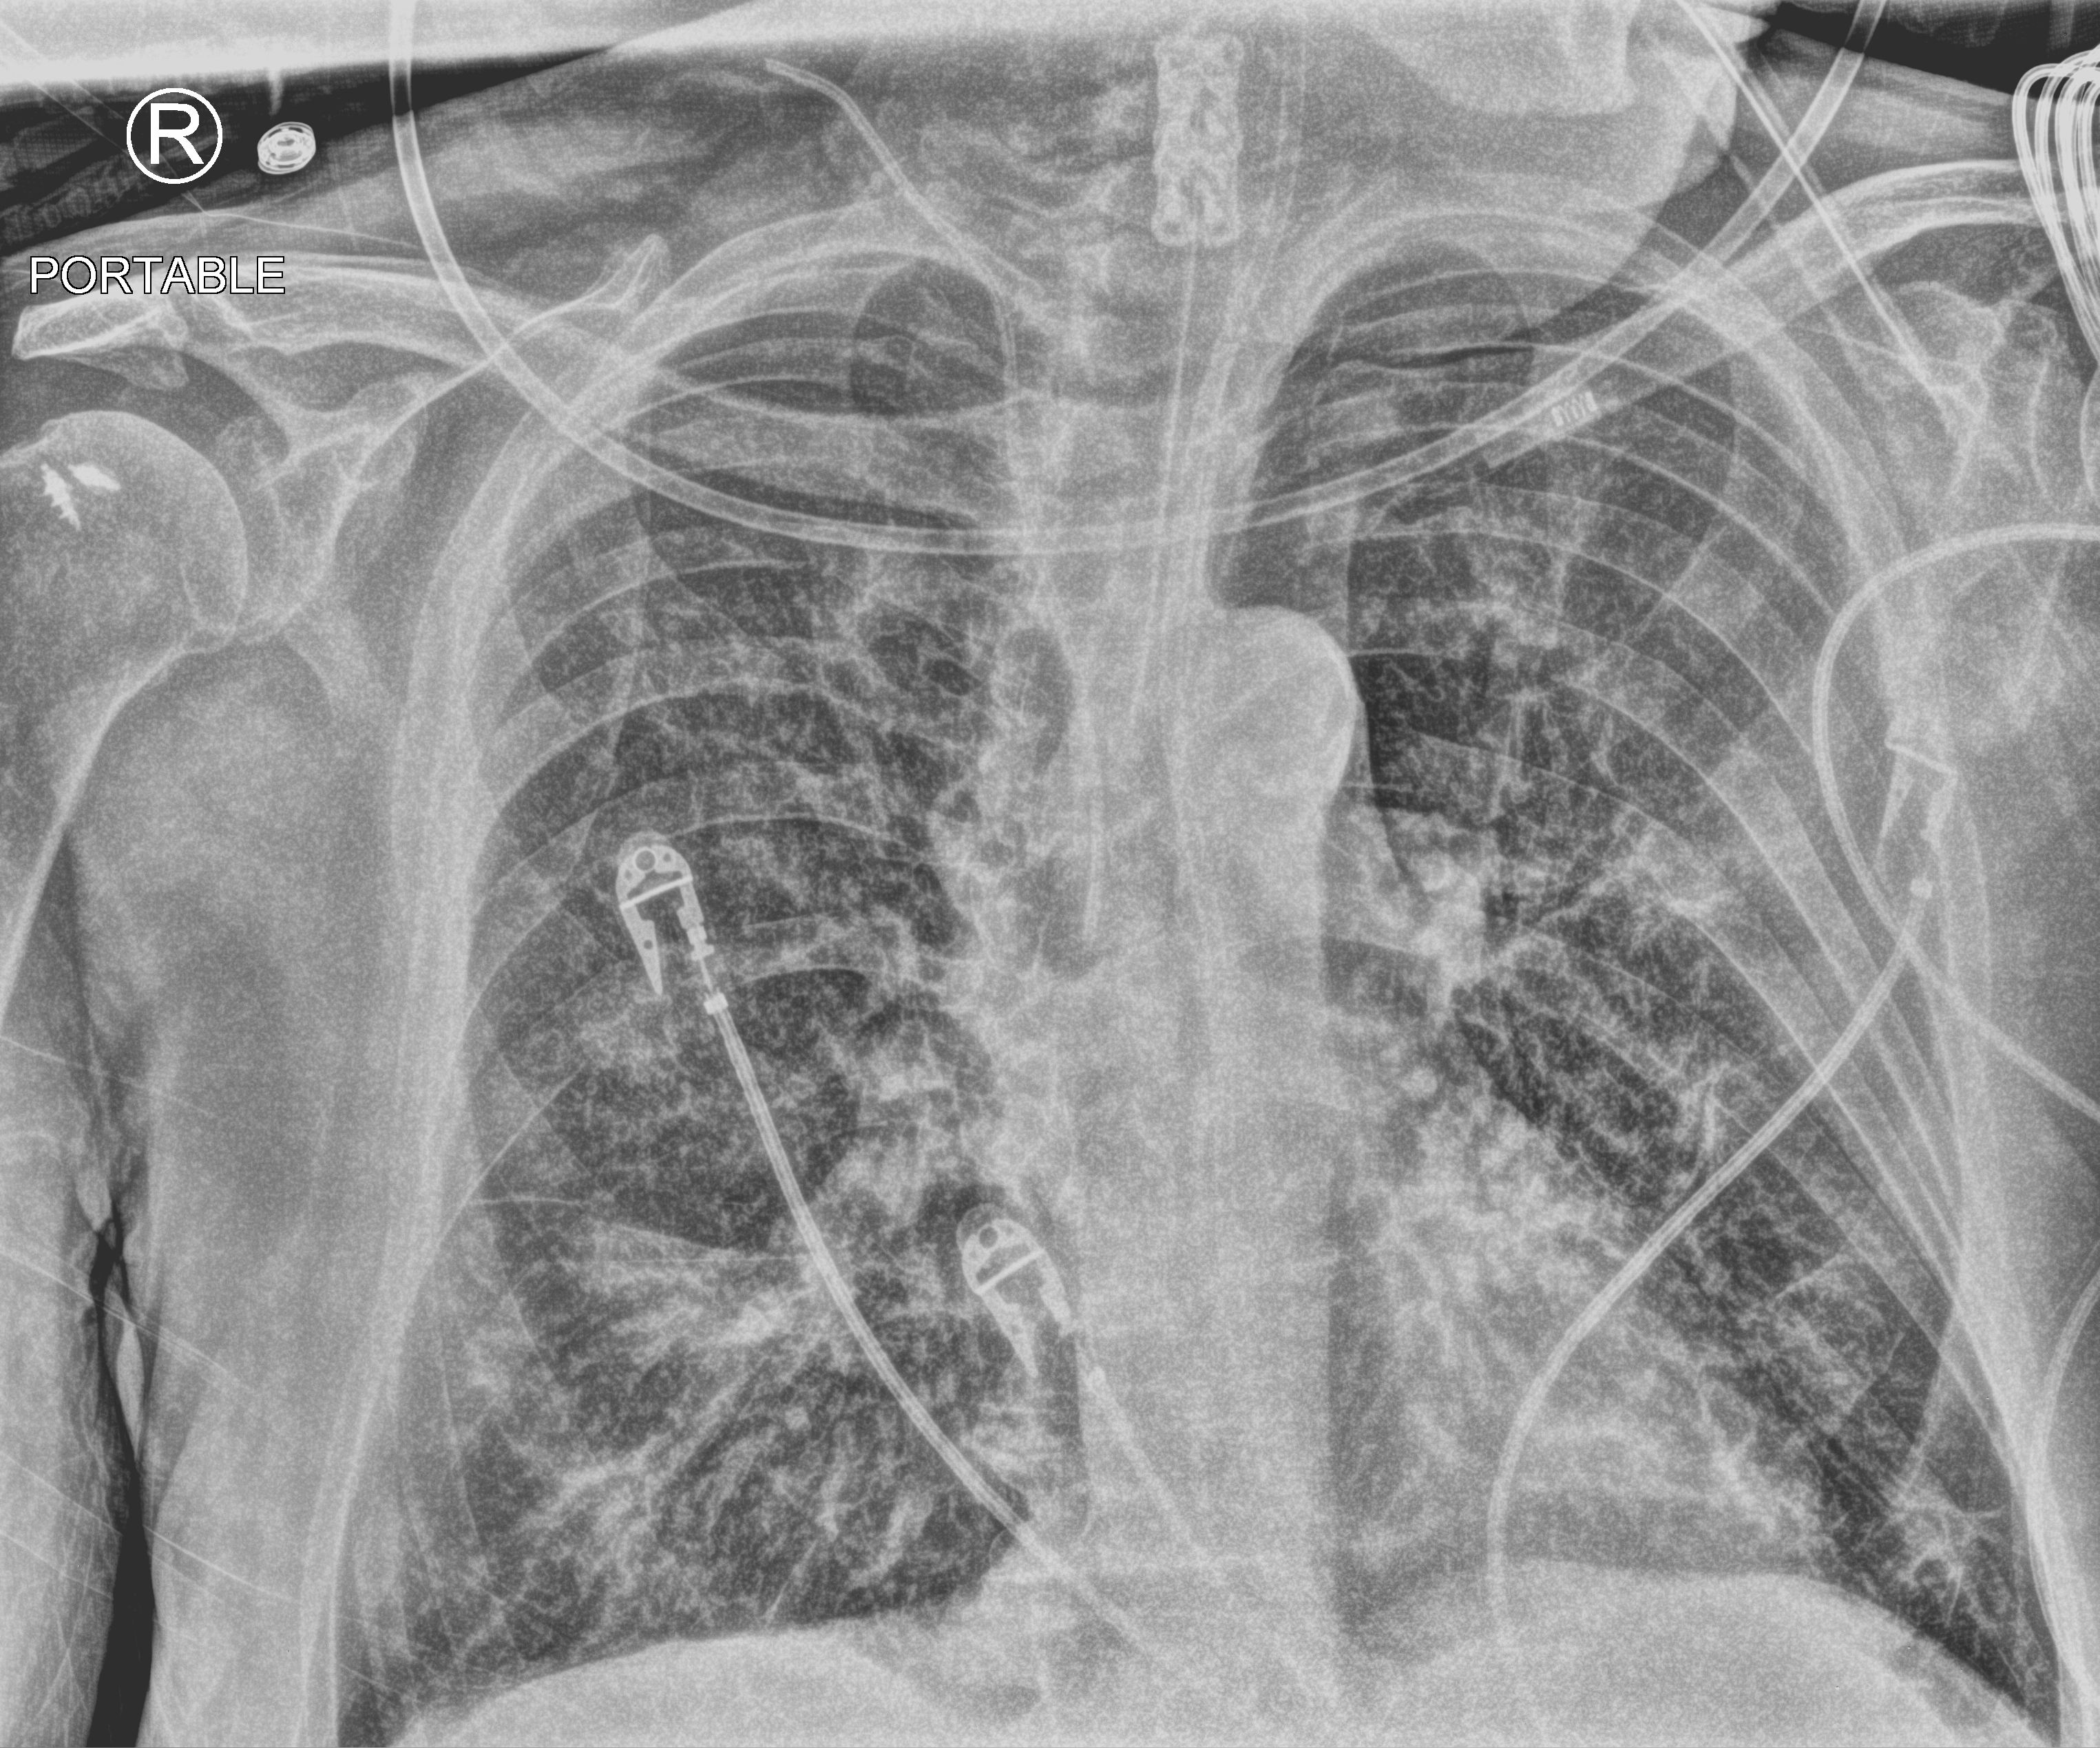
Portable chest radiograph; anteroposterior (AP) projection. Male patient hospitalised with COVID-19, age 75–90 years.
Hospital-stay facts (about this admission, not read from this image; timing relative to this image not recorded):
- mechanically ventilated during this hospital stay: yes
- smoking status (admission record): former